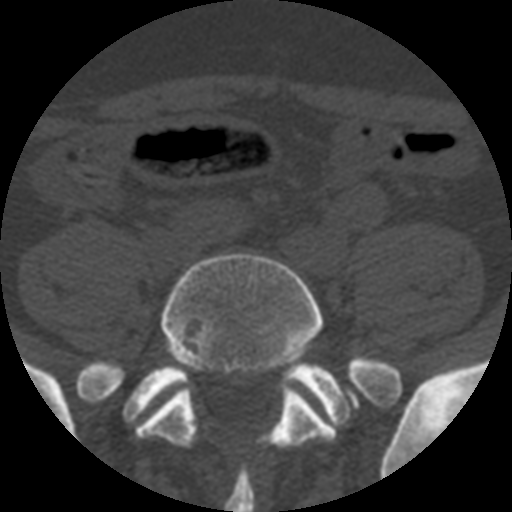
CT including the spine, one axial slice. Position 57 of 508 along the scan axis. Reconstruction kernel STANDARD. 120 kVp. Bone window (W 1800 / L 400 HU). 1.25 mm slice thickness. 512 × 512 image matrix. Patient age 57 years. Case-level facts recorded for this patient, not image findings: primary cancer: prostate.
Structures marked on this image (semi-automatically segmented with operator editing):
- L5 vertebra: box from (x=135, y=253) to (x=394, y=449) px